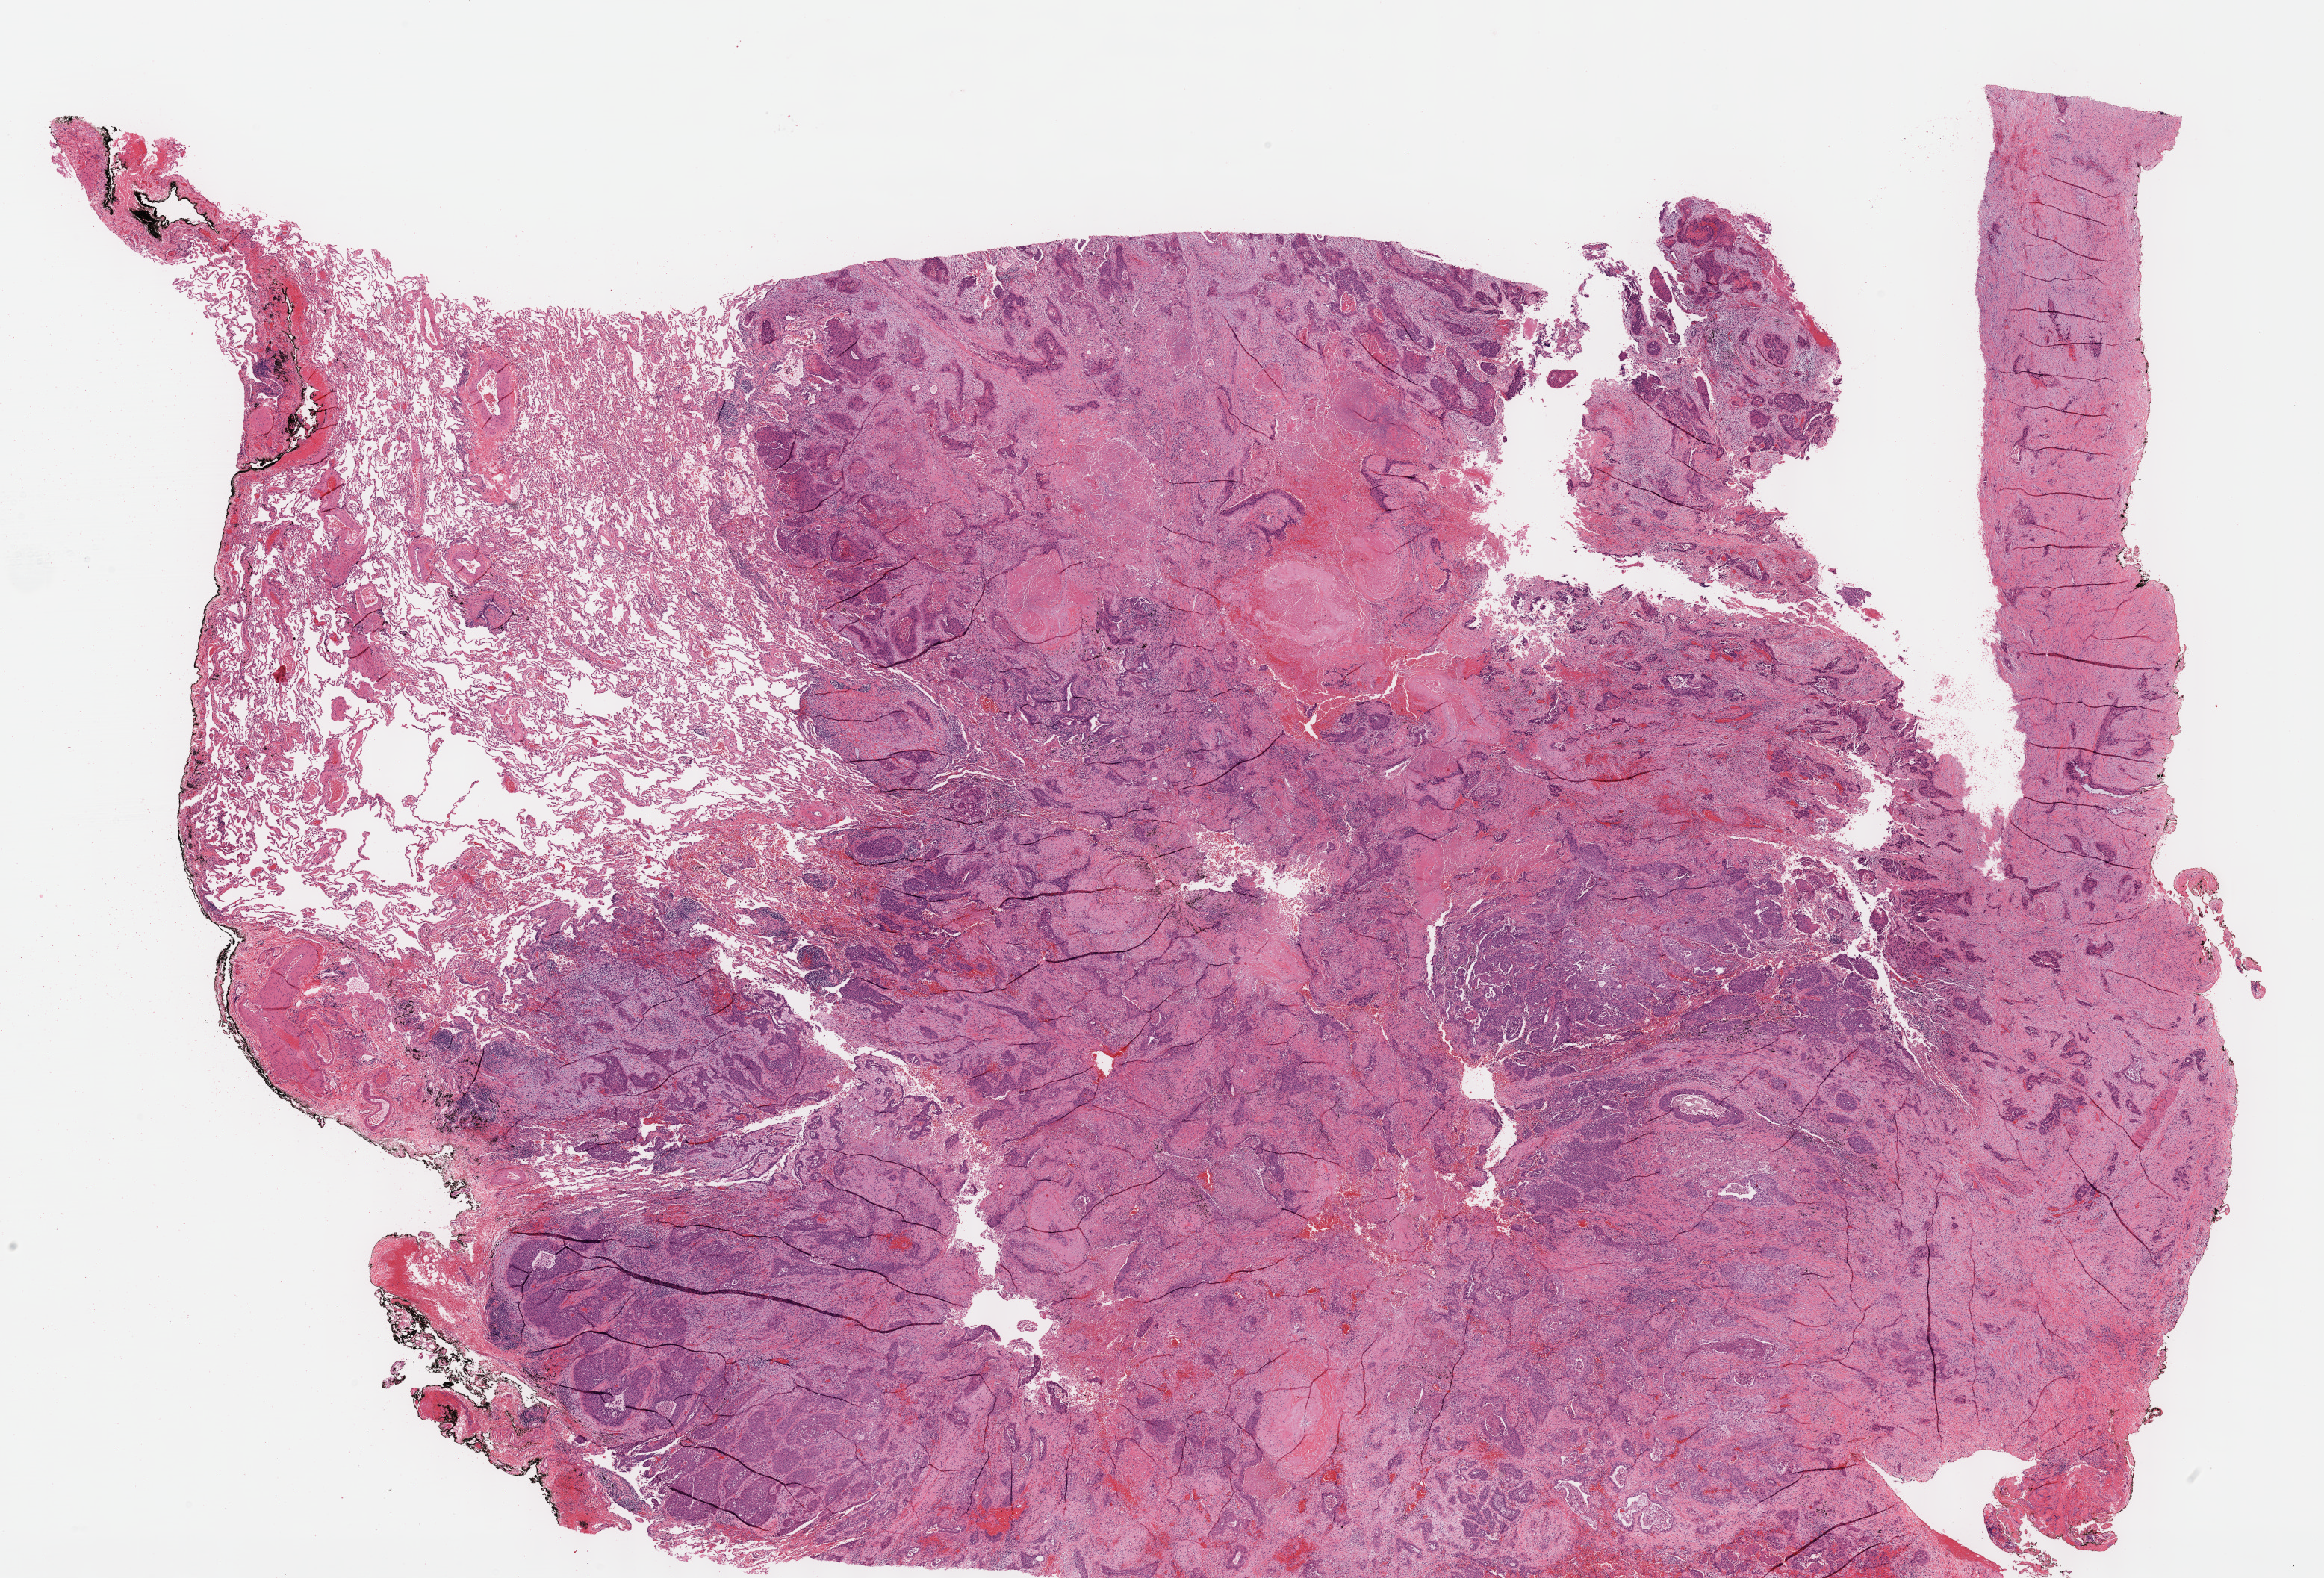
Whole-slide histology image, Hematoxylin and eosin (H&E) stained — shown as a low-resolution overview of the whole scanned area (about 25.1 x 17.1 mm, acquisition: 40x scan), formalin-fixed paraffin-embedded (FFPE) diagnostic section, sample: primary tumour, lung. Male patient; age at initial diagnosis 84 years.
TNM: T4 N1 MX. Pathologic diagnosis: Squamous cell carcinoma, NOS (upper lobe, lung). Laterality: left. AJCC pathologic stage: IIIA (7th edition).